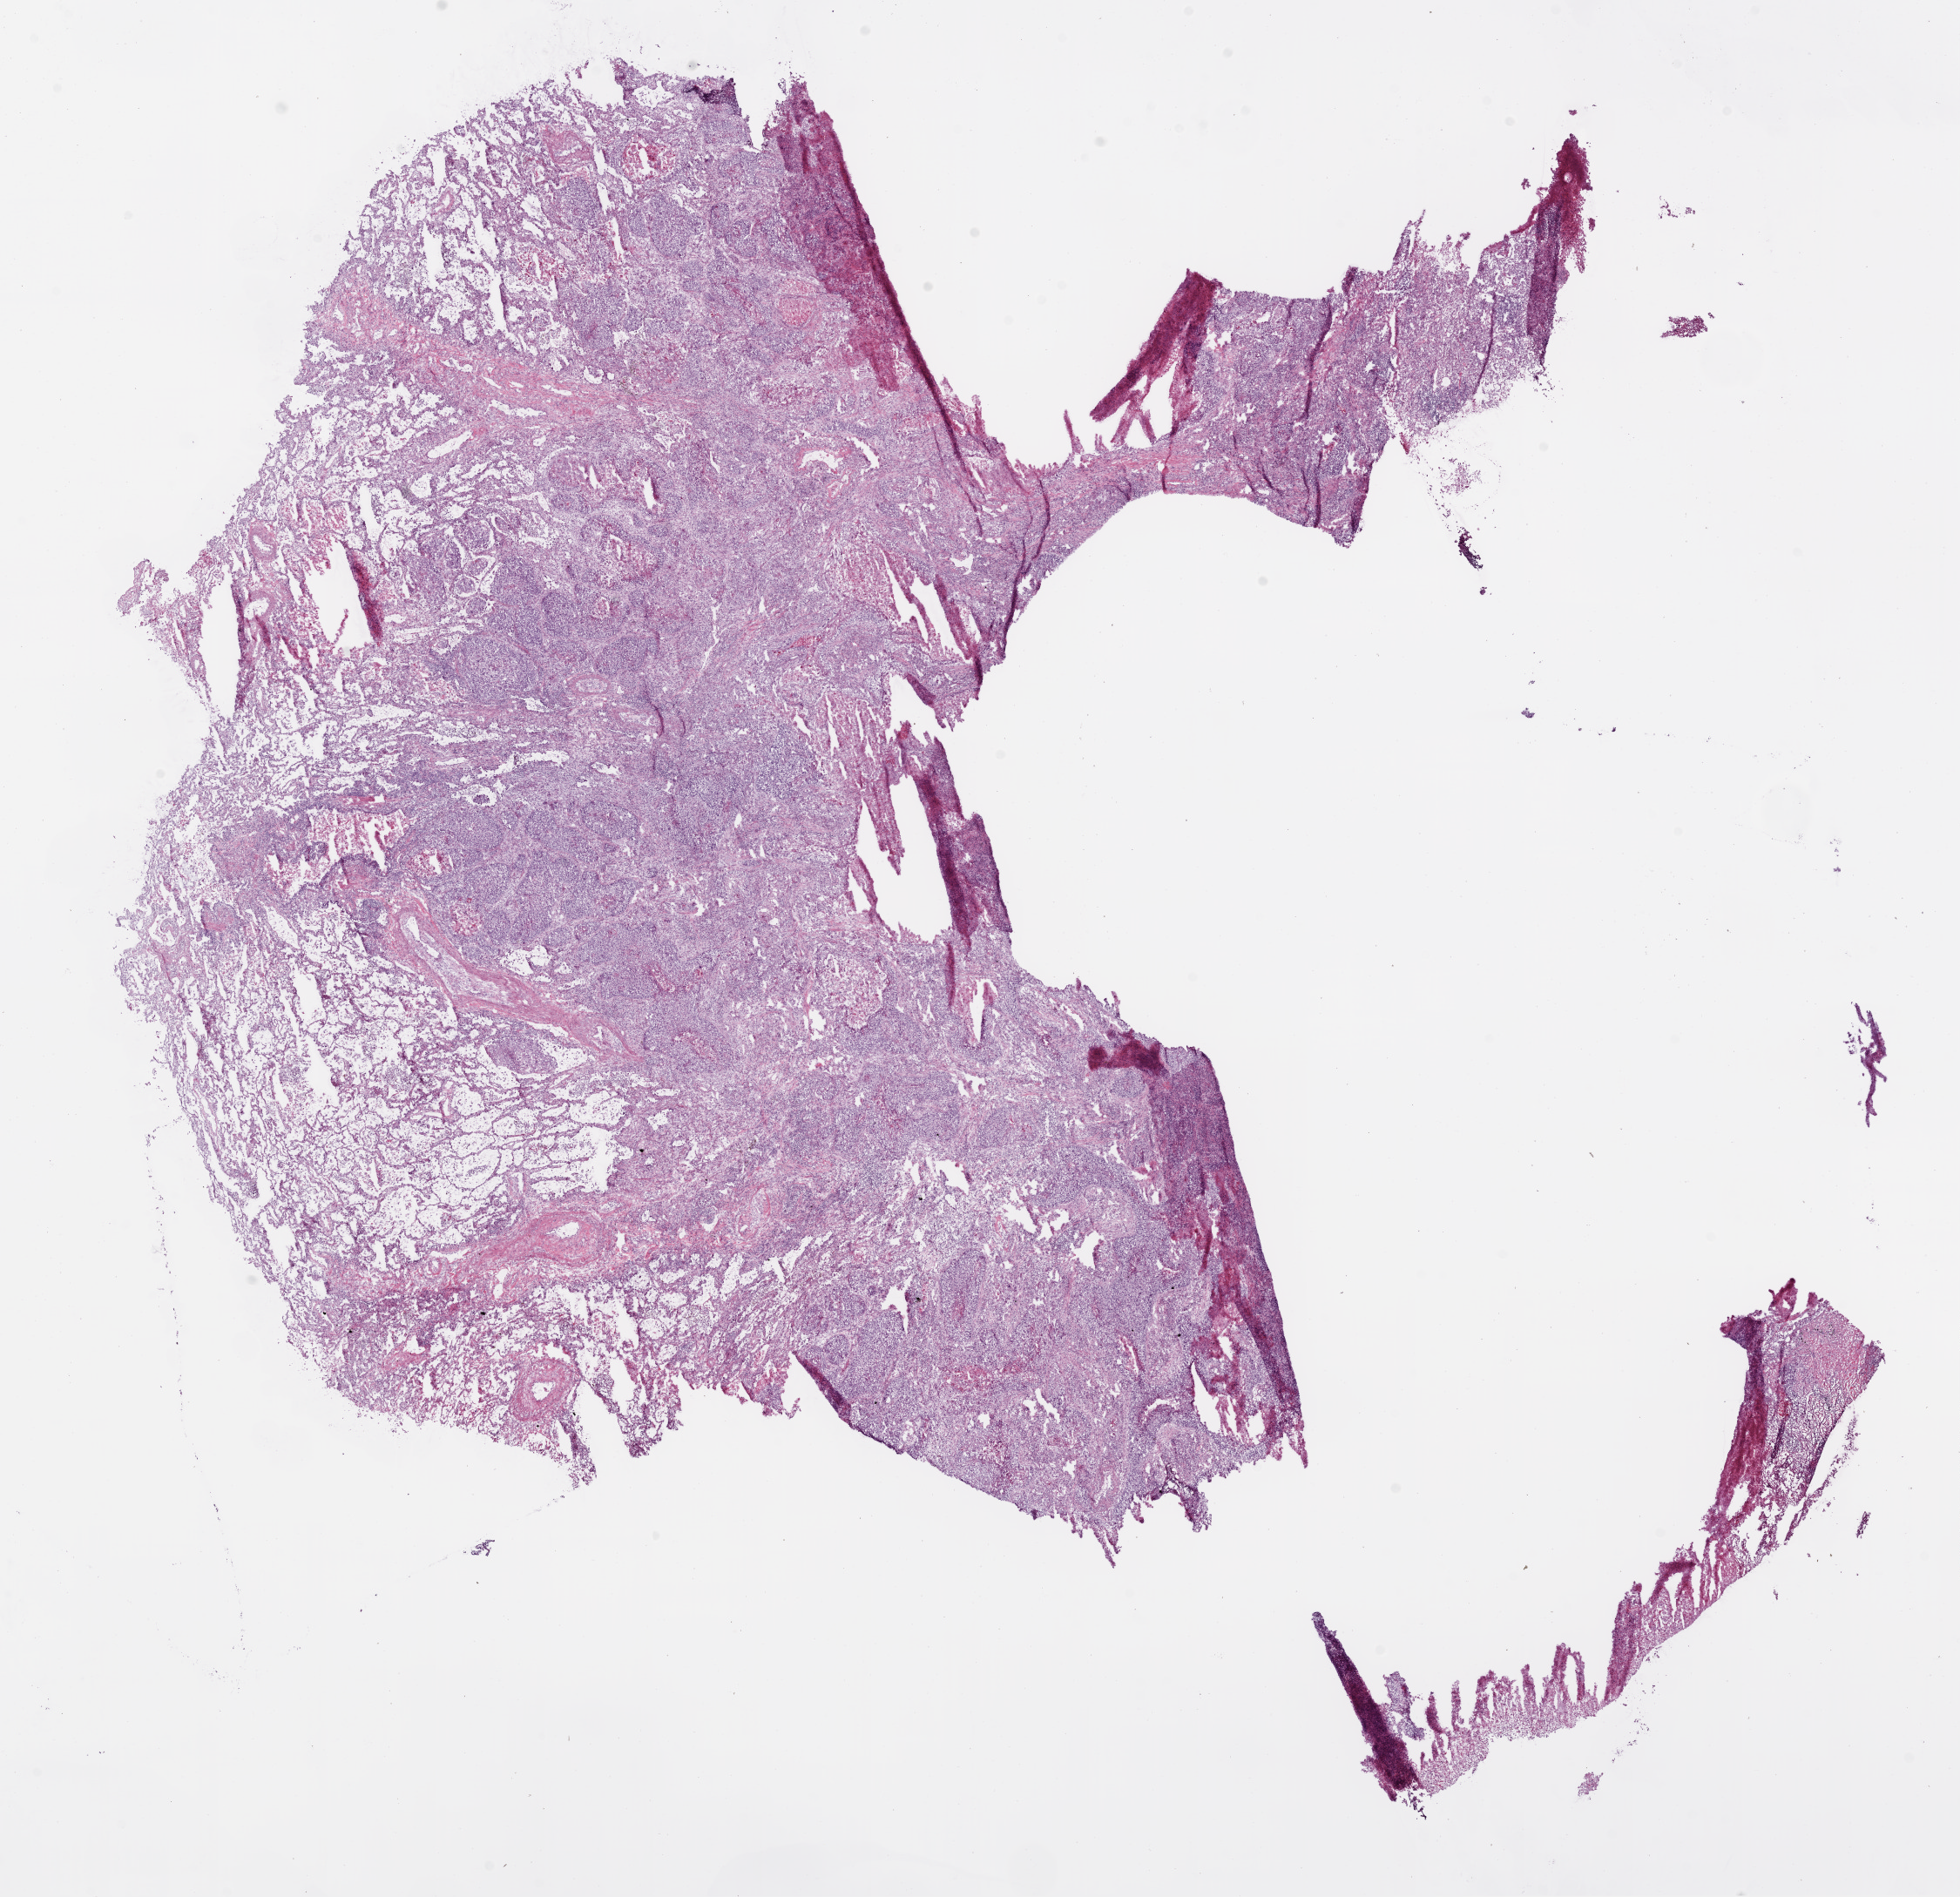
Digitized H&E-stained tissue section (whole slide) — a low-resolution overview of the entire scanned area, about 18.1 x 17.5 mm (acquisition: 20x scan). Frozen section from the bottom of the tissue portion. Lung, primary tumour sample. Male patient; age at initial diagnosis 79 years. Slide review estimates, as recorded: tumour cells 45%, tumour nuclei 70%, normal cells 30%, stromal cells 10%, necrosis 15%.
Laterality: right. Diagnosis: Squamous cell carcinoma, NOS (lower lobe, lung). AJCC pathologic stage: IB.